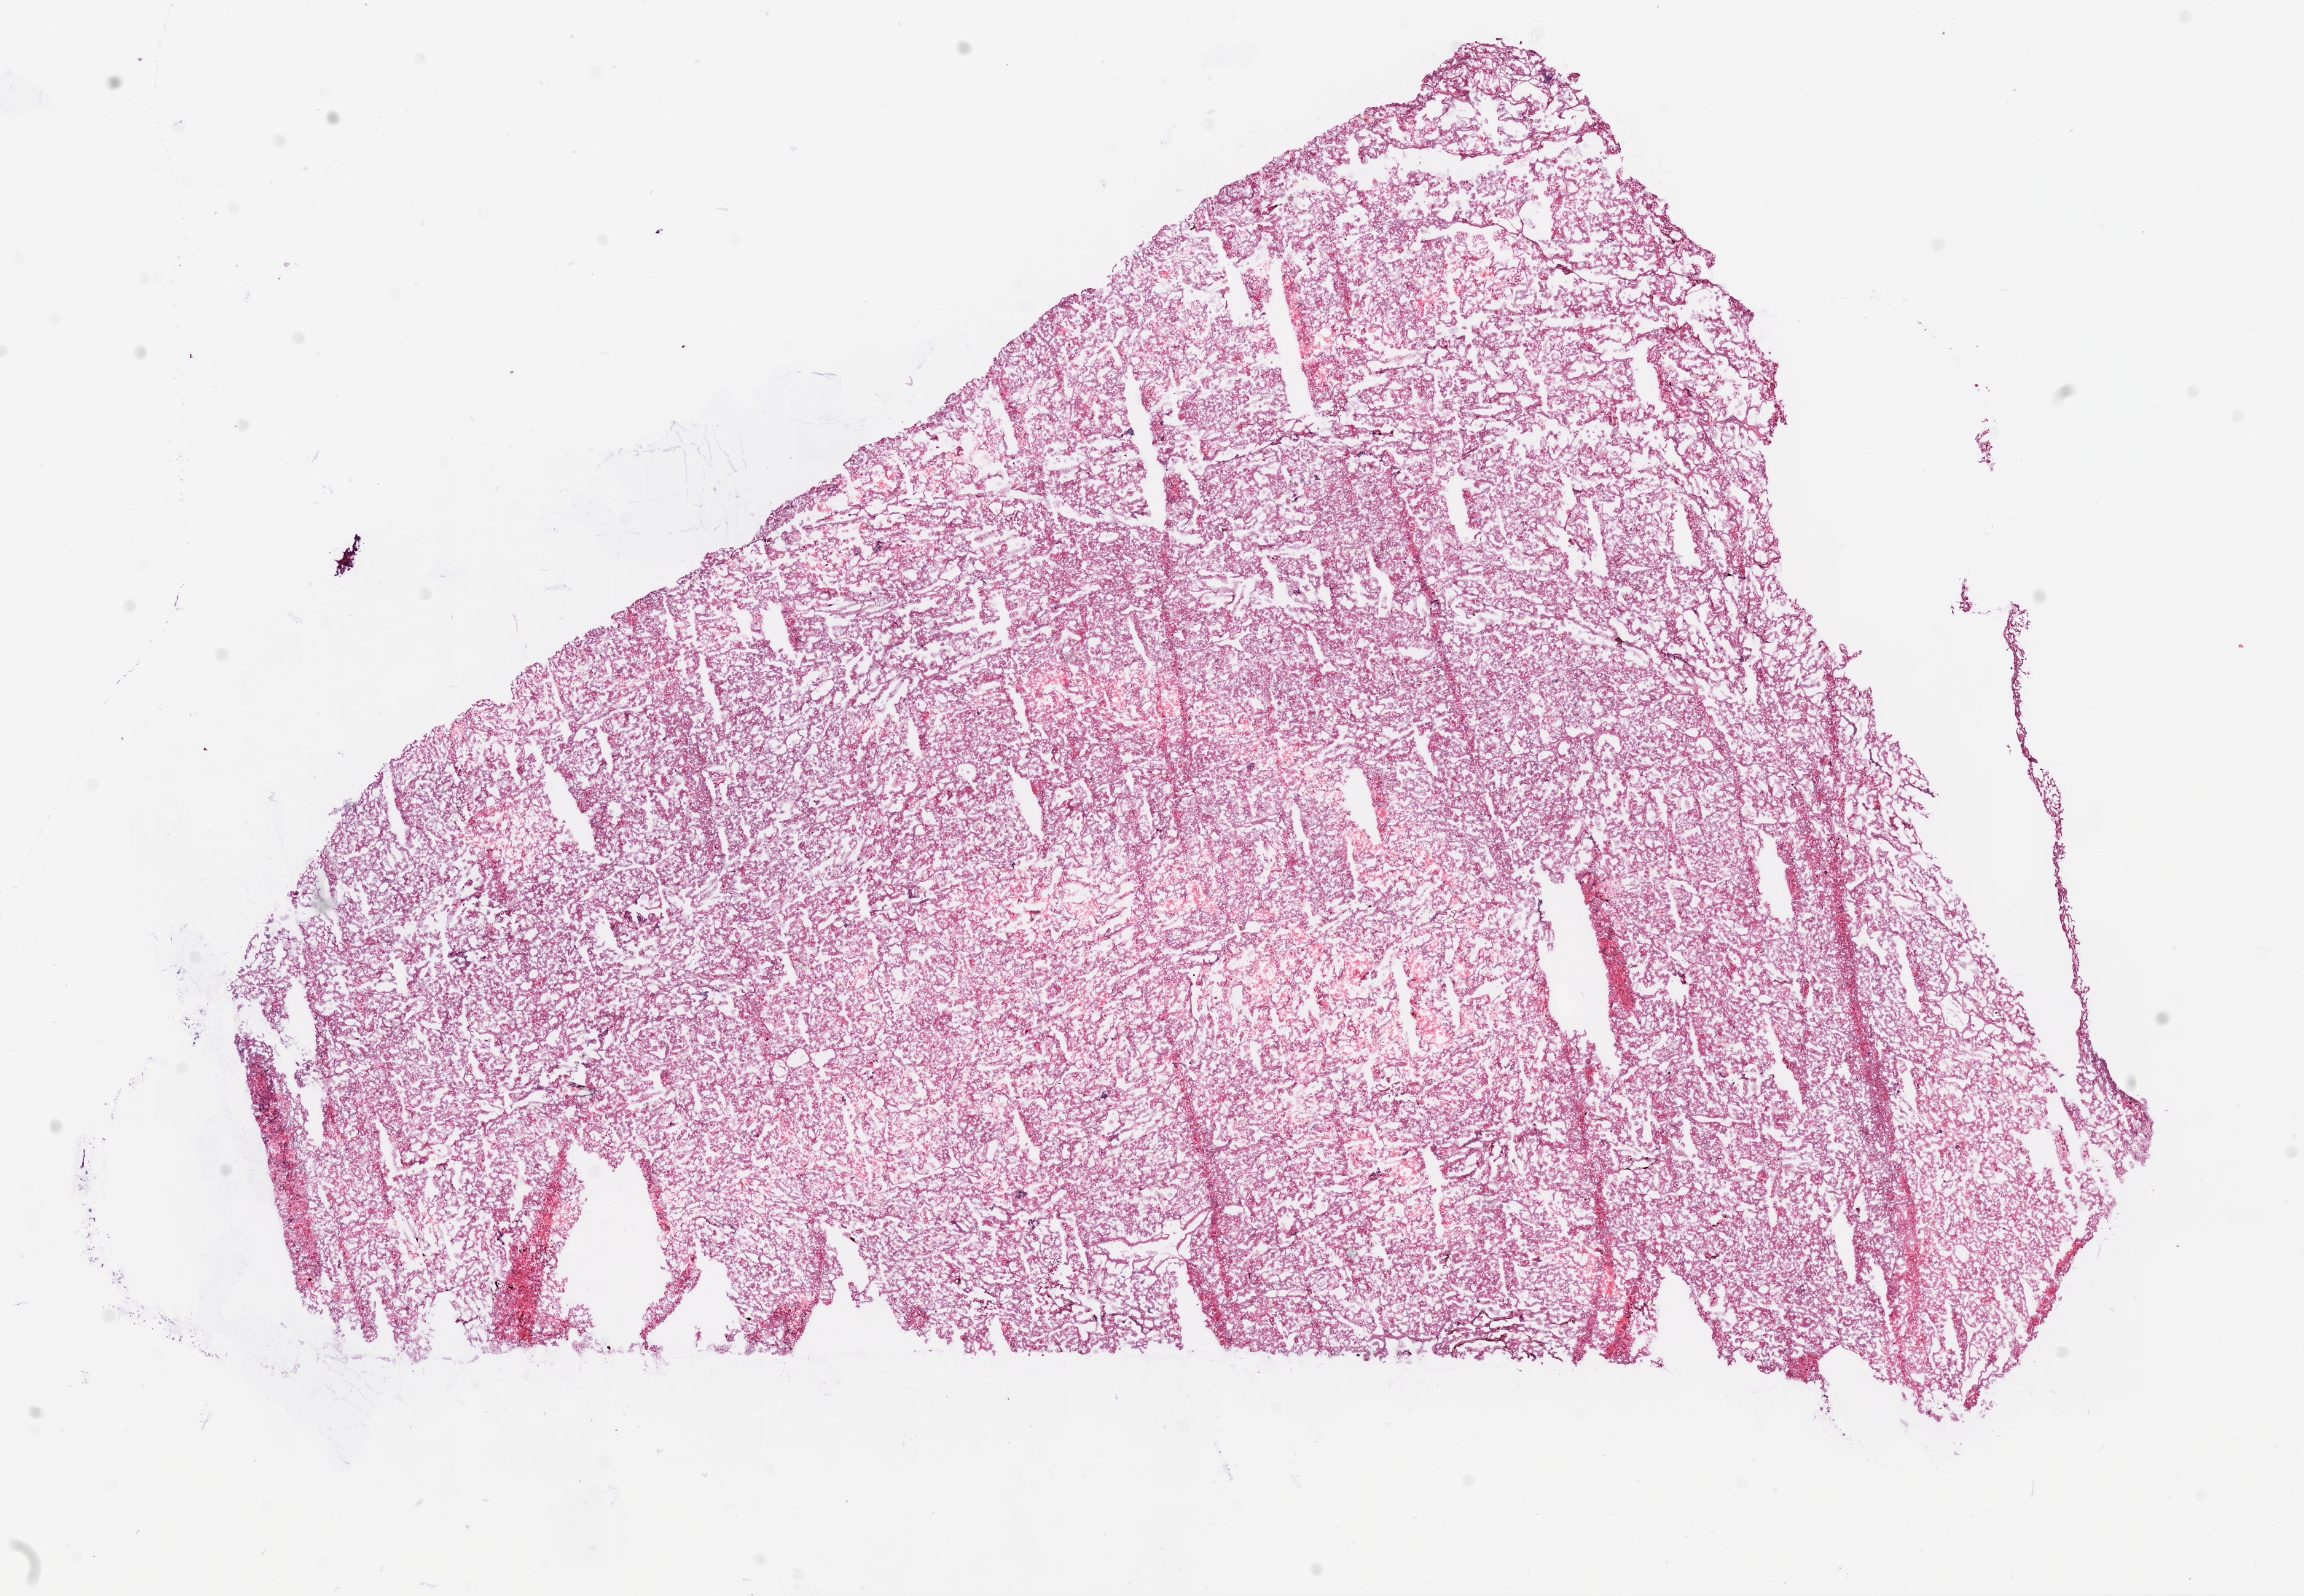
Digitized Hematoxylin and eosin (H&E) stained tissue section (whole slide), whole scanned area (about 15.0 x 10.4 mm, from a 20x scan) shown as a low-resolution overview. Frozen section. Sample: primary tumour, kidney. Patient: male, age at initial diagnosis 58 years. Histologic grade: G3 (poorly differentiated). Slide review estimates, as recorded: tumour nuclei 85%, normal cells 0%, stromal cells 5%, necrosis 1%.
• AJCC pathologic stage: I (6th edition)
• histologic diagnosis: Clear cell adenocarcinoma, NOS
• laterality: left